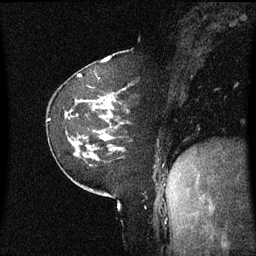
Breast MRI (dynamic contrast-enhanced), one sagittal slice; position 17 of 60 along the scan axis; dynamic contrast-enhanced series, image 2 of 3 at this slice position (ordered by acquisition); 1.5 T; TE 4.2 ms, TR 8.4 ms; 2.2 mm slice thickness; 256 × 256 image matrix, field of view 220 × 220 mm. Patient: female, 60 years. From the clinical record (not read from this slice): setting: breast cancer imaged before/during neoadjuvant chemotherapy; receptor status: triple-negative.
Outlined on this slice (semi-automatic segmentation, software-assisted and operator-edited):
- analysis volume of interest (the breast-tissue region the enhancement analysis was run in; not a lesion): bounding box (x1, y1, x2, y2) in pixels: (65, 98, 125, 161)
- tumour enhancement mask (voxels above the 70 % enhancement threshold inside the analysis volume of interest): (101, 108, 113, 141)